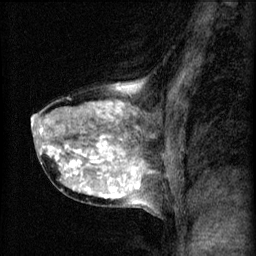
Breast MRI (dynamic contrast-enhanced), one sagittal slice. Slice 34 of 60 in the series (ordered by position). 3 images stored at this slice position (order not interpretable as contrast timing). 1.5 T. TE 4.2 ms, TR 8.2 ms. 256 × 256 image matrix, field of view 180 × 180 mm. Female patient, age 40 years.
Outlined on this slice (semi-automatically segmented with operator editing):
- analysis volume of interest (the breast-tissue region the enhancement analysis was run in; not a lesion): box from (x=31, y=80) to (x=167, y=211) px
- tumour enhancement mask (voxels above the 70 % enhancement threshold inside the analysis volume of interest): (x=32, y=86)–(x=152, y=199)